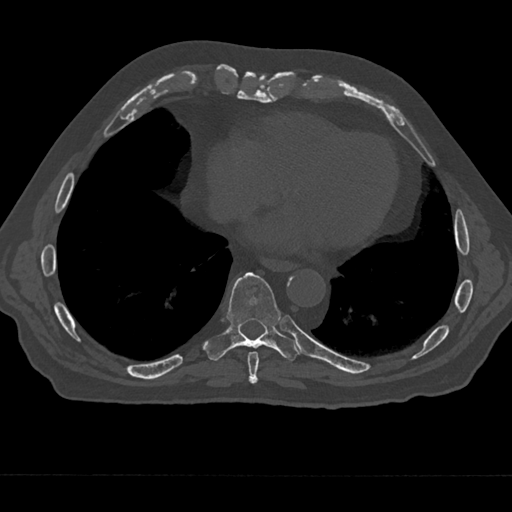
CT including the spine, one axial slice. Reconstruction kernel Br40s/3. 120 kVp. Bone window (W 1800 / L 400 HU). 0.5 mm slice thickness. 512 × 512 image matrix. Male patient, age 75 years. From the clinical record (not read from this slice): primary cancer: renal.
Annotated regions visible in this slice (semi-automatically segmented with operator editing):
- T8 vertebra: bounding box (x1, y1, x2, y2) in pixels: (247, 351, 259, 384)
- T9 vertebra: (204, 272, 300, 361)